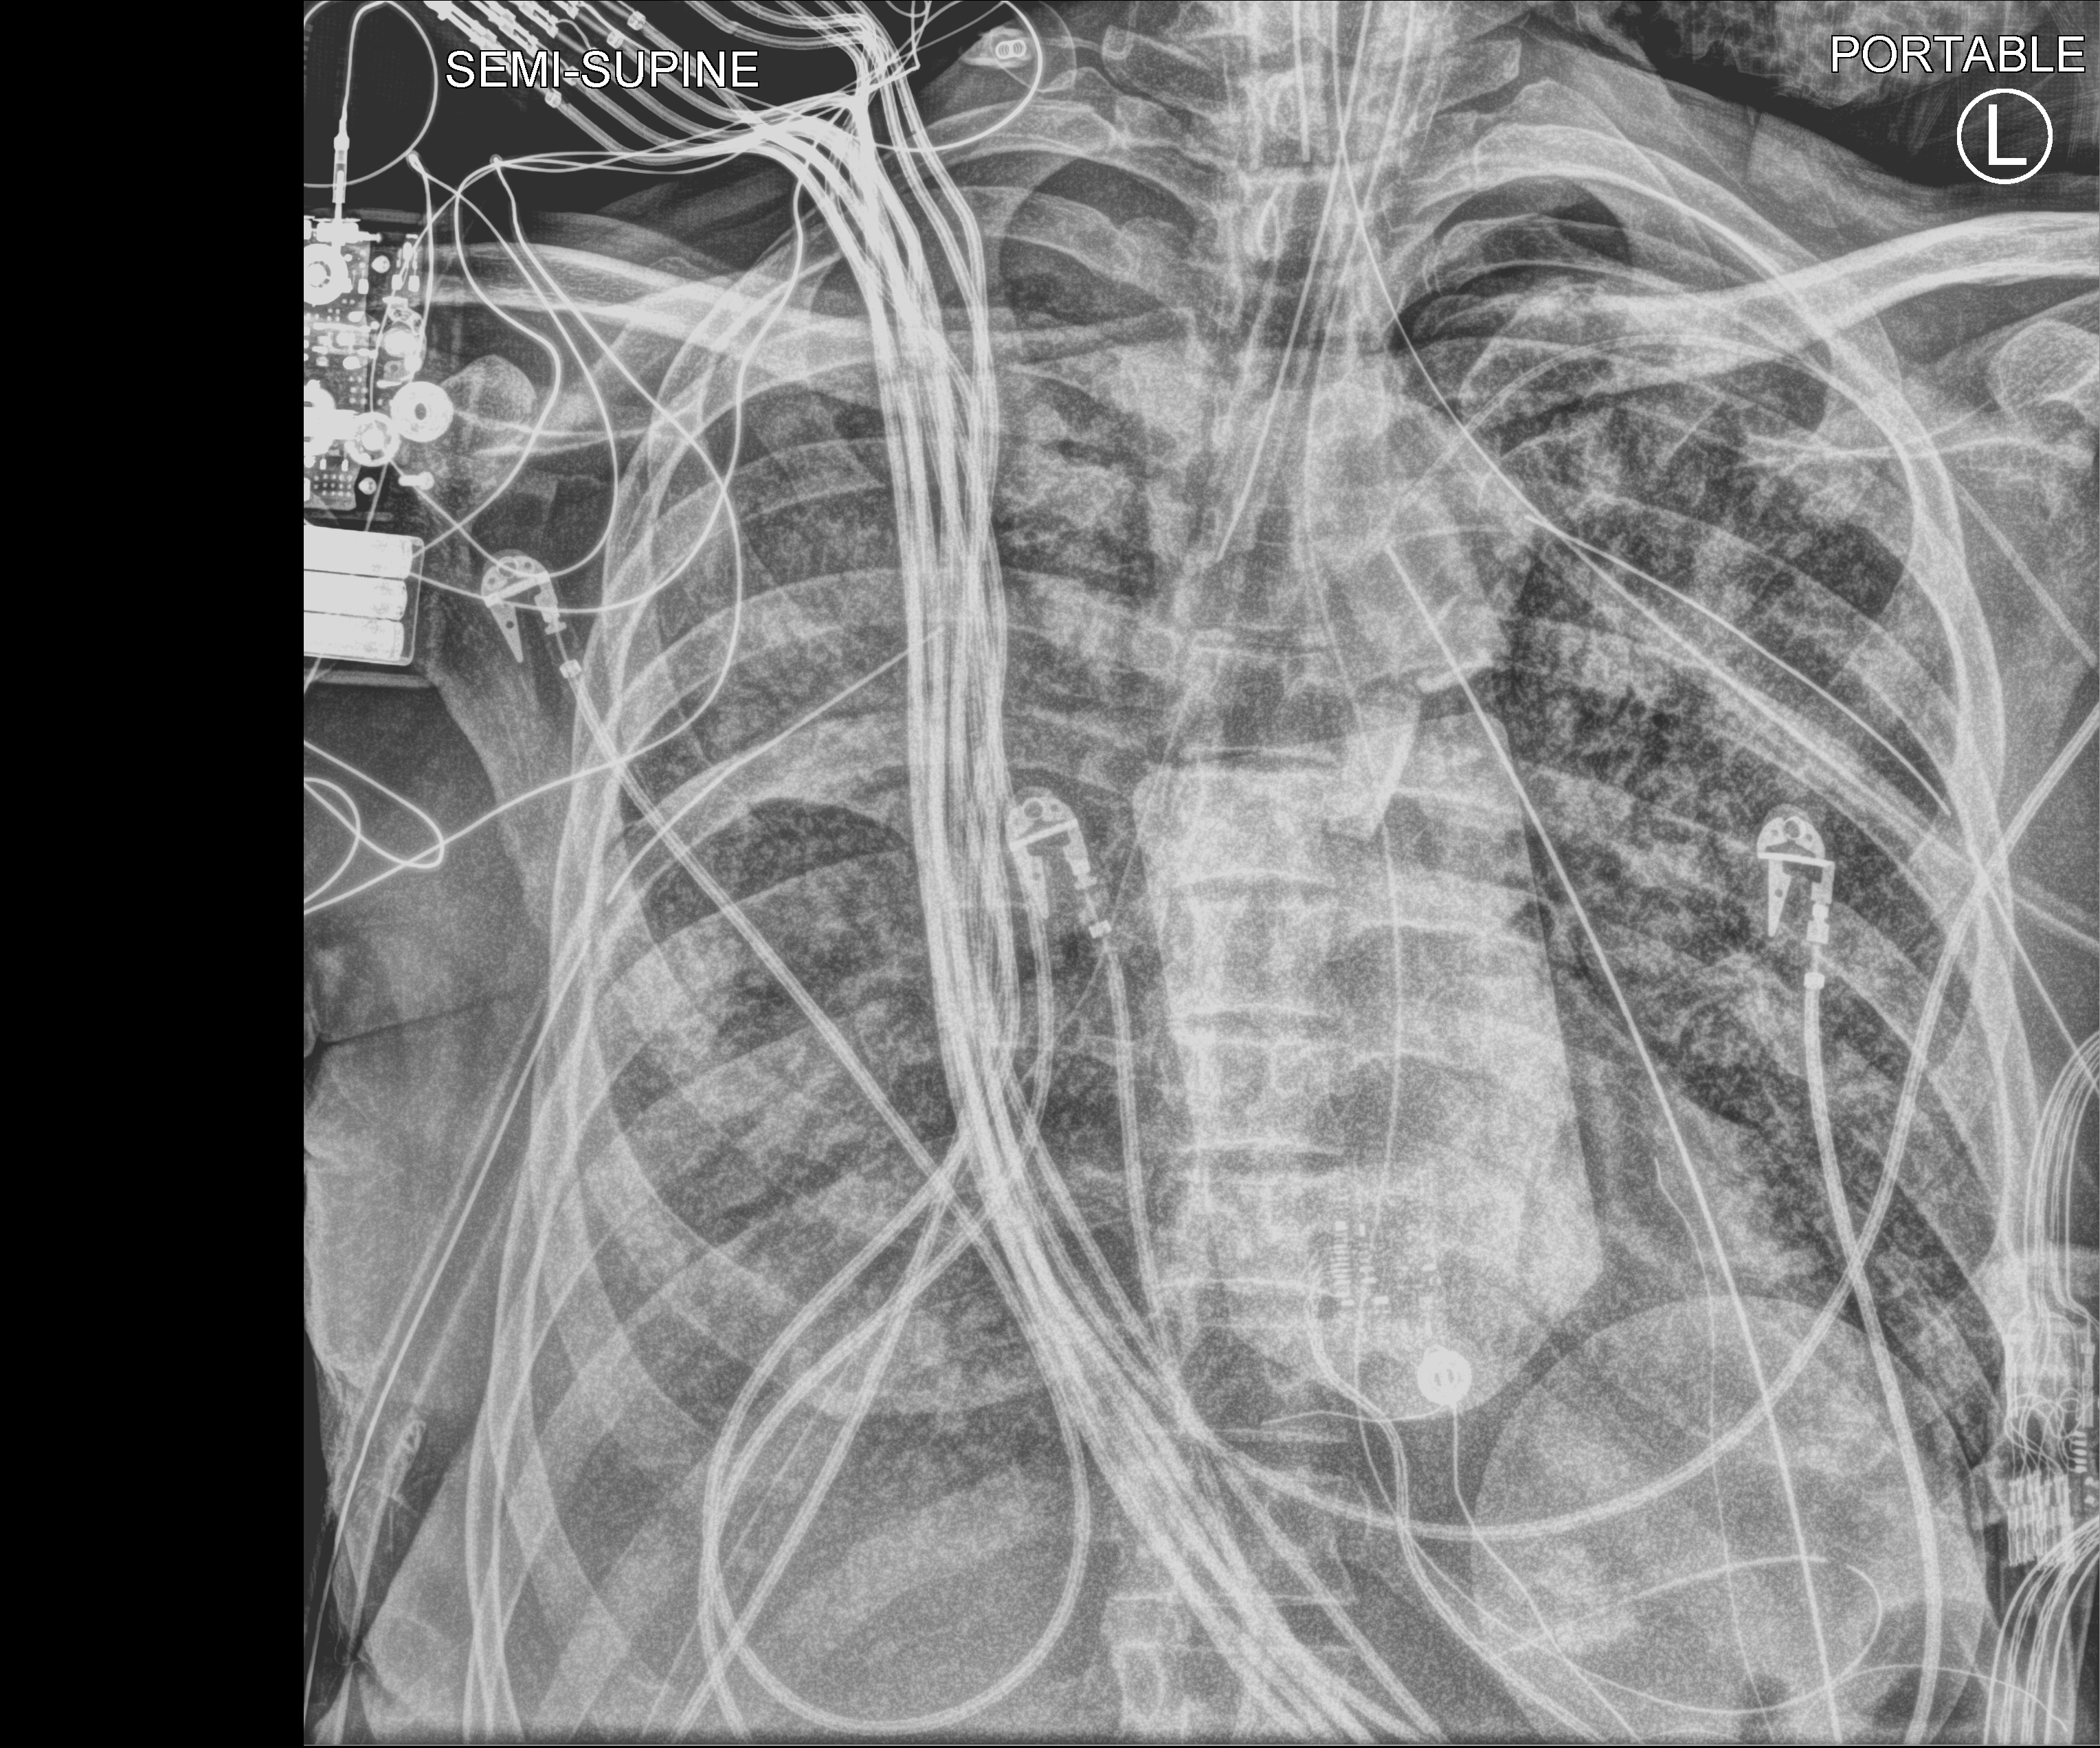
Bedside chest radiograph (computed radiography), anteroposterior (AP) projection. Patient hospitalised with COVID-19; male, aged 60–74 years.
Hospital-stay facts (about this admission, not read from this image; timing relative to this image not recorded): admitted to intensive care during this hospital stay: yes; mechanically ventilated during this hospital stay: yes.